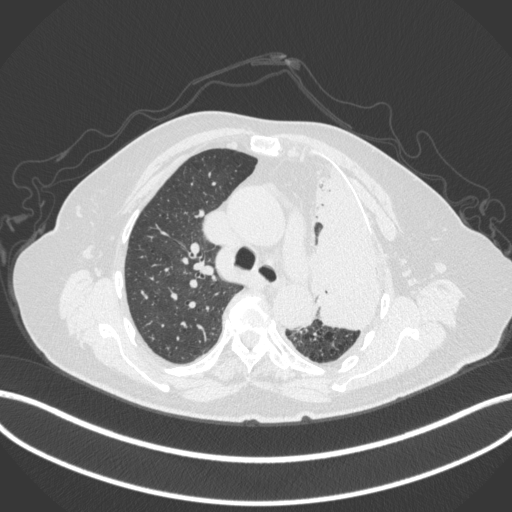
Chest CT, one axial slice. Slice 274 of 399 in the series (ordered by position). 120 kVp. Lung window (W 1500 / L -600 HU). 1 mm slice thickness. 512 × 512 image matrix, field of view 400 × 400 mm. Patient: female, 75 years. Case-level facts recorded for this patient, not image findings: clinical TNM (as recorded): T3 N3 M1.
Structures marked on this image (rectangle marked by the reading radiologist):
- lung tumour (recorded histology: adenocarcinoma): bounding box <311,153,394,332> (left, top, right, bottom; pixels)